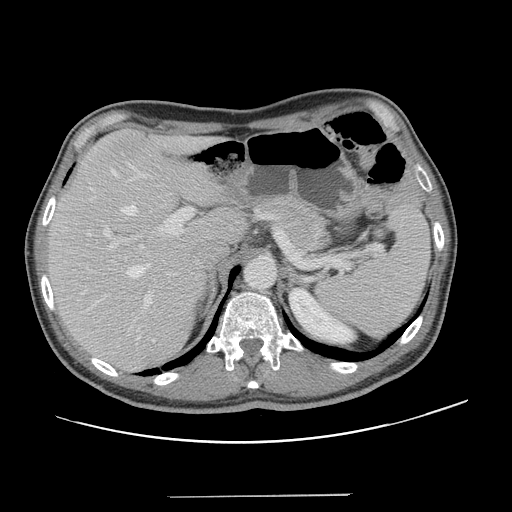
Contrast-enhanced abdominal CT, one axial slice; position 91 of 131 along the scan axis; 120 kVp; soft-tissue window (W 400 / L 40 HU); 2.5 mm slice thickness; 512 × 512 image matrix, field of view 403 × 403 mm. Male patient, age 60 years. From the clinical record (not read from this slice): diagnosis: colorectal cancer liver metastases, imaged before liver resection; multiple liver metastases: no; largest metastasis: 2.5 cm; chemotherapy before resection: no.
Annotated regions visible in this slice (outlined manually by an expert reader):
- hepatic veins: box from (x=87, y=169) to (x=150, y=311) px
- liver: (x=47, y=129)–(x=244, y=371)
- planned liver remnant (the part of the liver to remain after resection): (x=47, y=129)–(x=244, y=354)
- portal vein (with intrahepatic branches): (x=103, y=162)–(x=194, y=305)